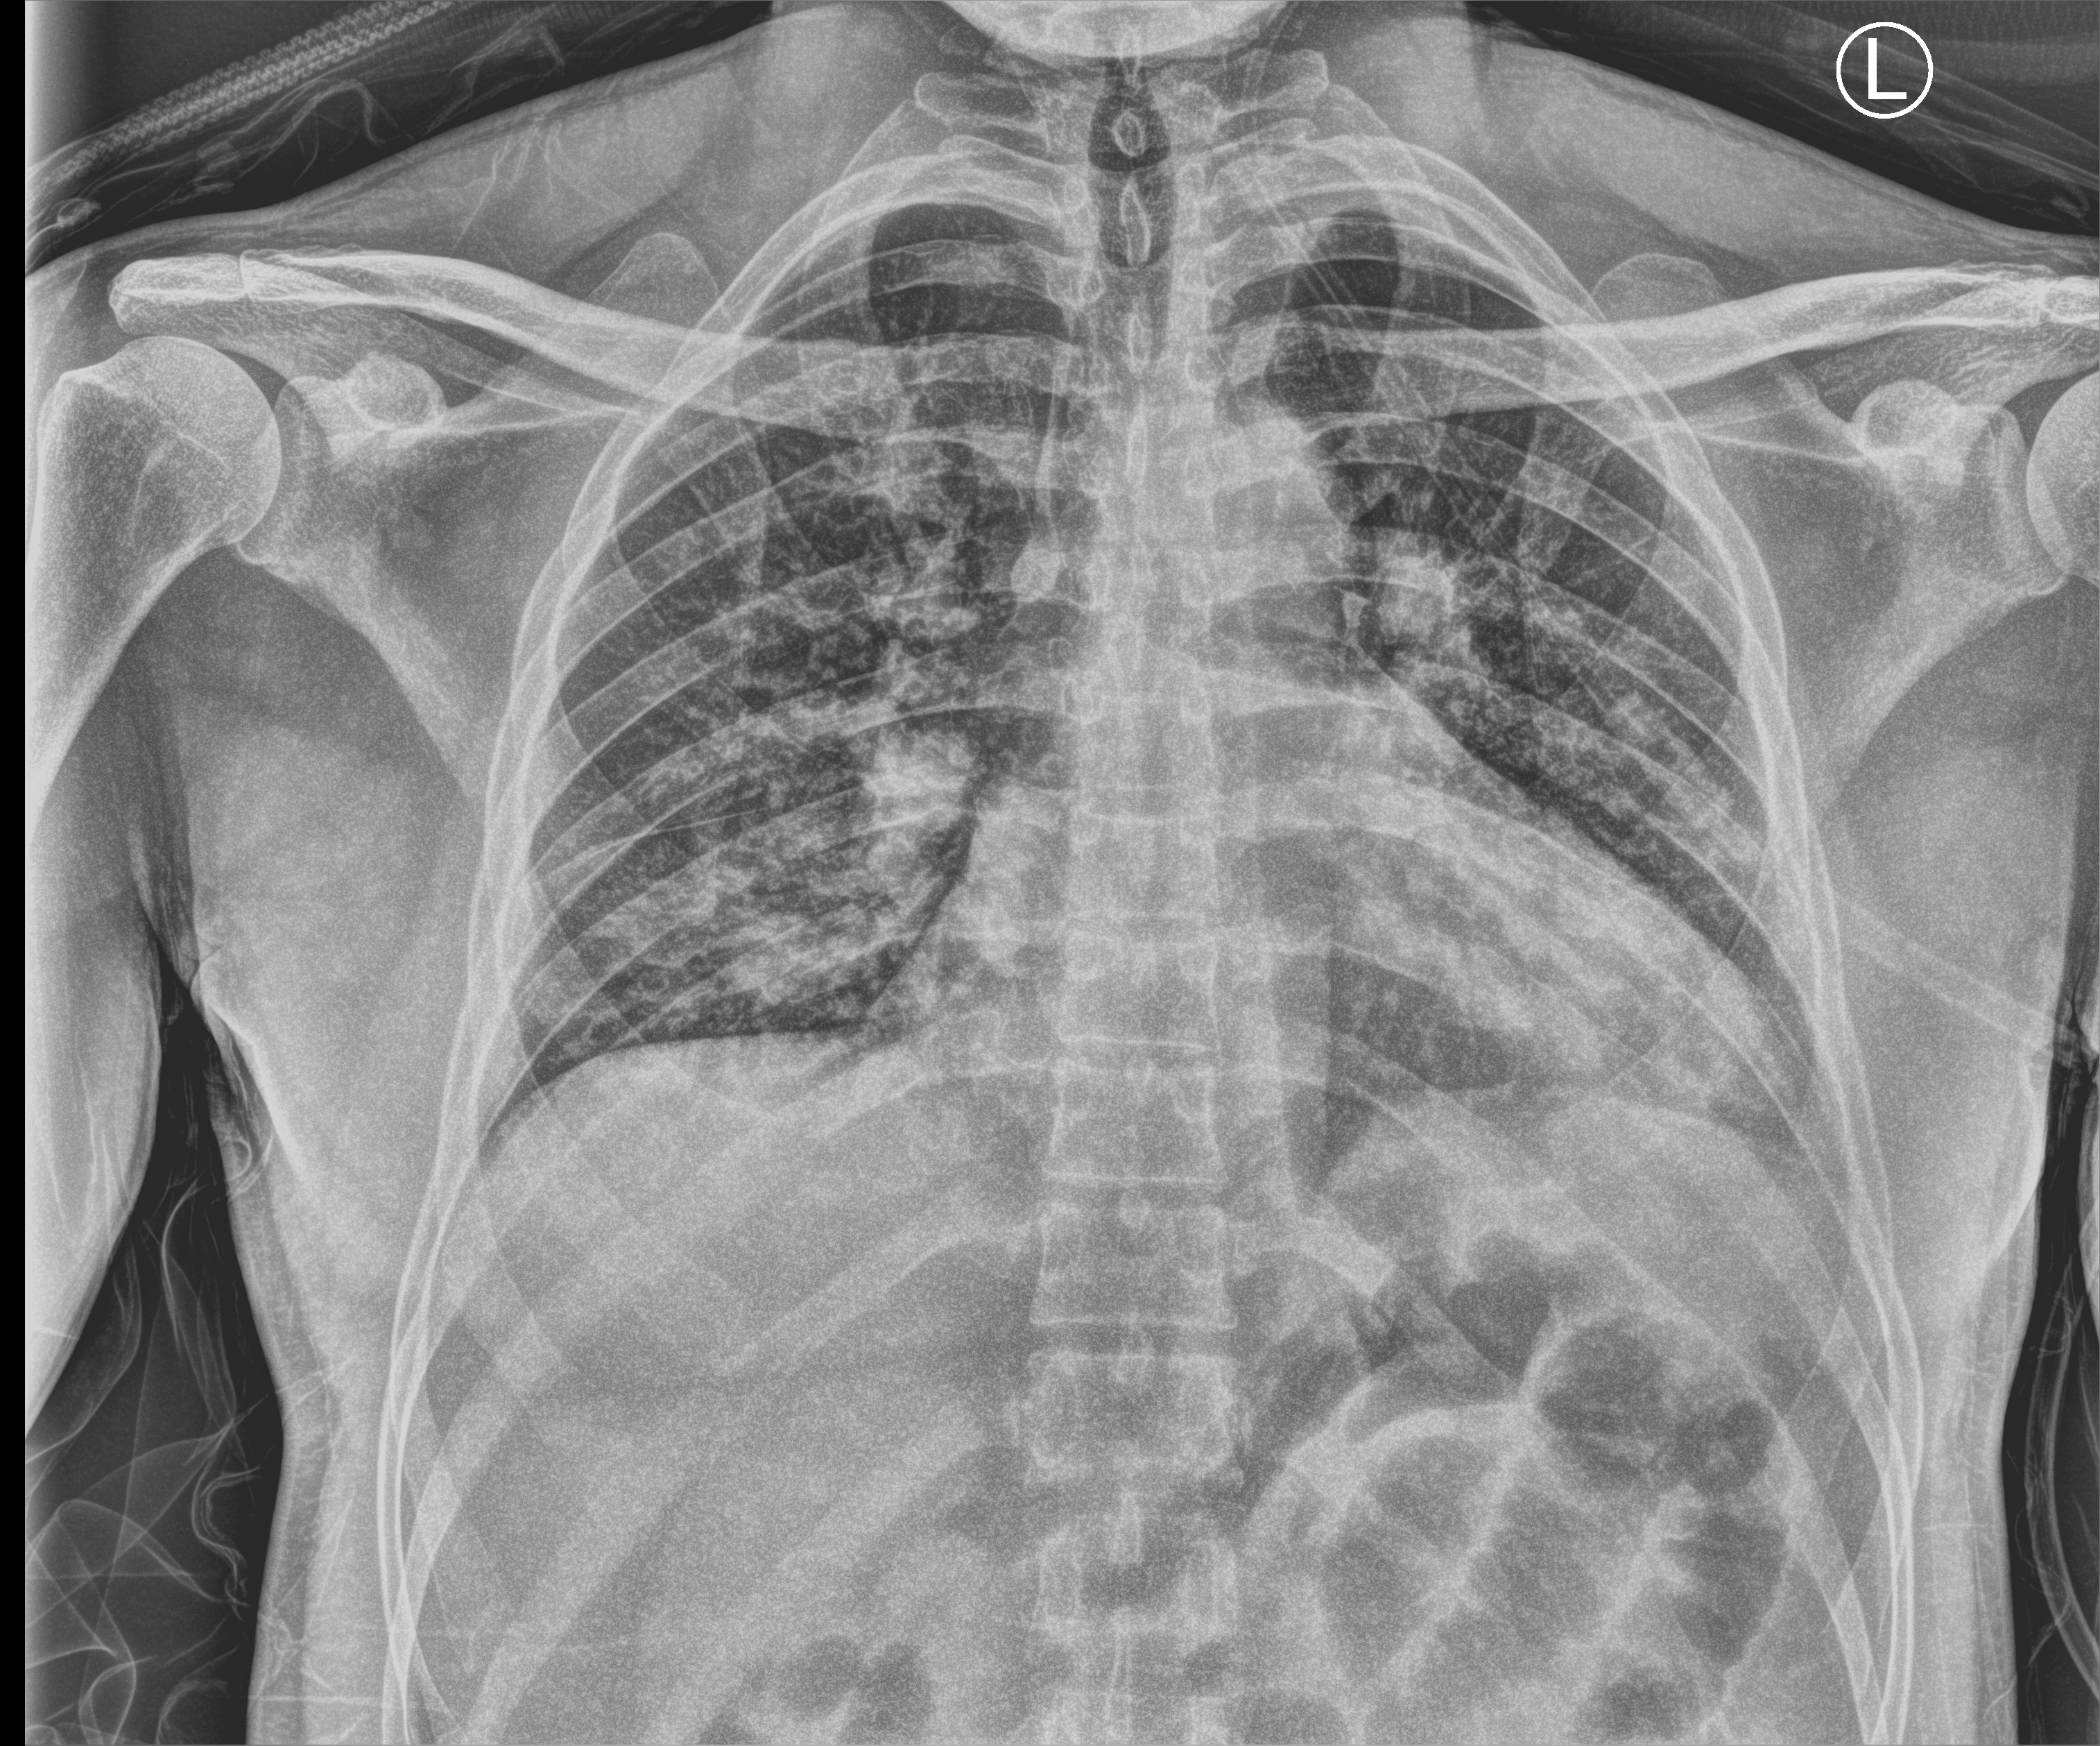
Bedside chest radiograph (computed radiography), anteroposterior (AP) projection. Male patient hospitalised with COVID-19, age 18–59 years.
Admission-level facts for this patient (not findings on this image; timing relative to this image not recorded):
- hypertension (admission record): no